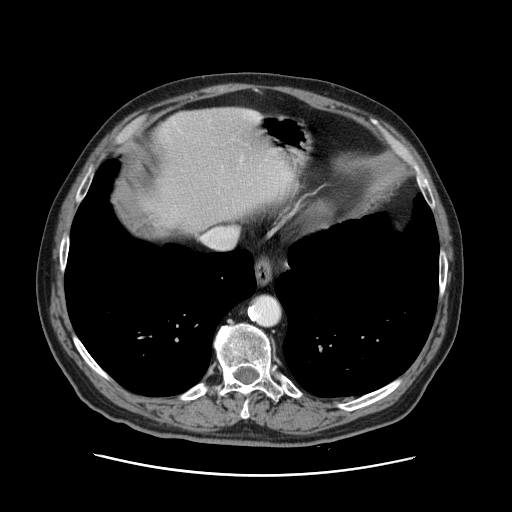
Contrast-enhanced abdominal CT, one axial slice; slice 114 of 141 in the series (ordered by position); 120 kVp; intravenous contrast given; soft-tissue window (W 400 / L 40 HU); 512 × 512 image matrix, field of view 395 × 395 mm. Male patient, age 72 years. From the clinical record (not read from this slice): diagnosis: colorectal cancer liver metastases, imaged before liver resection; multiple liver metastases: yes; largest metastasis: 5.4 cm; chemotherapy before resection: yes.
Outlined on this slice (outlined manually by an expert reader):
- liver: bounding box (x1, y1, x2, y2) in pixels: (148, 107, 283, 234)
- planned liver remnant (the part of the liver to remain after resection): (154, 107, 288, 234)